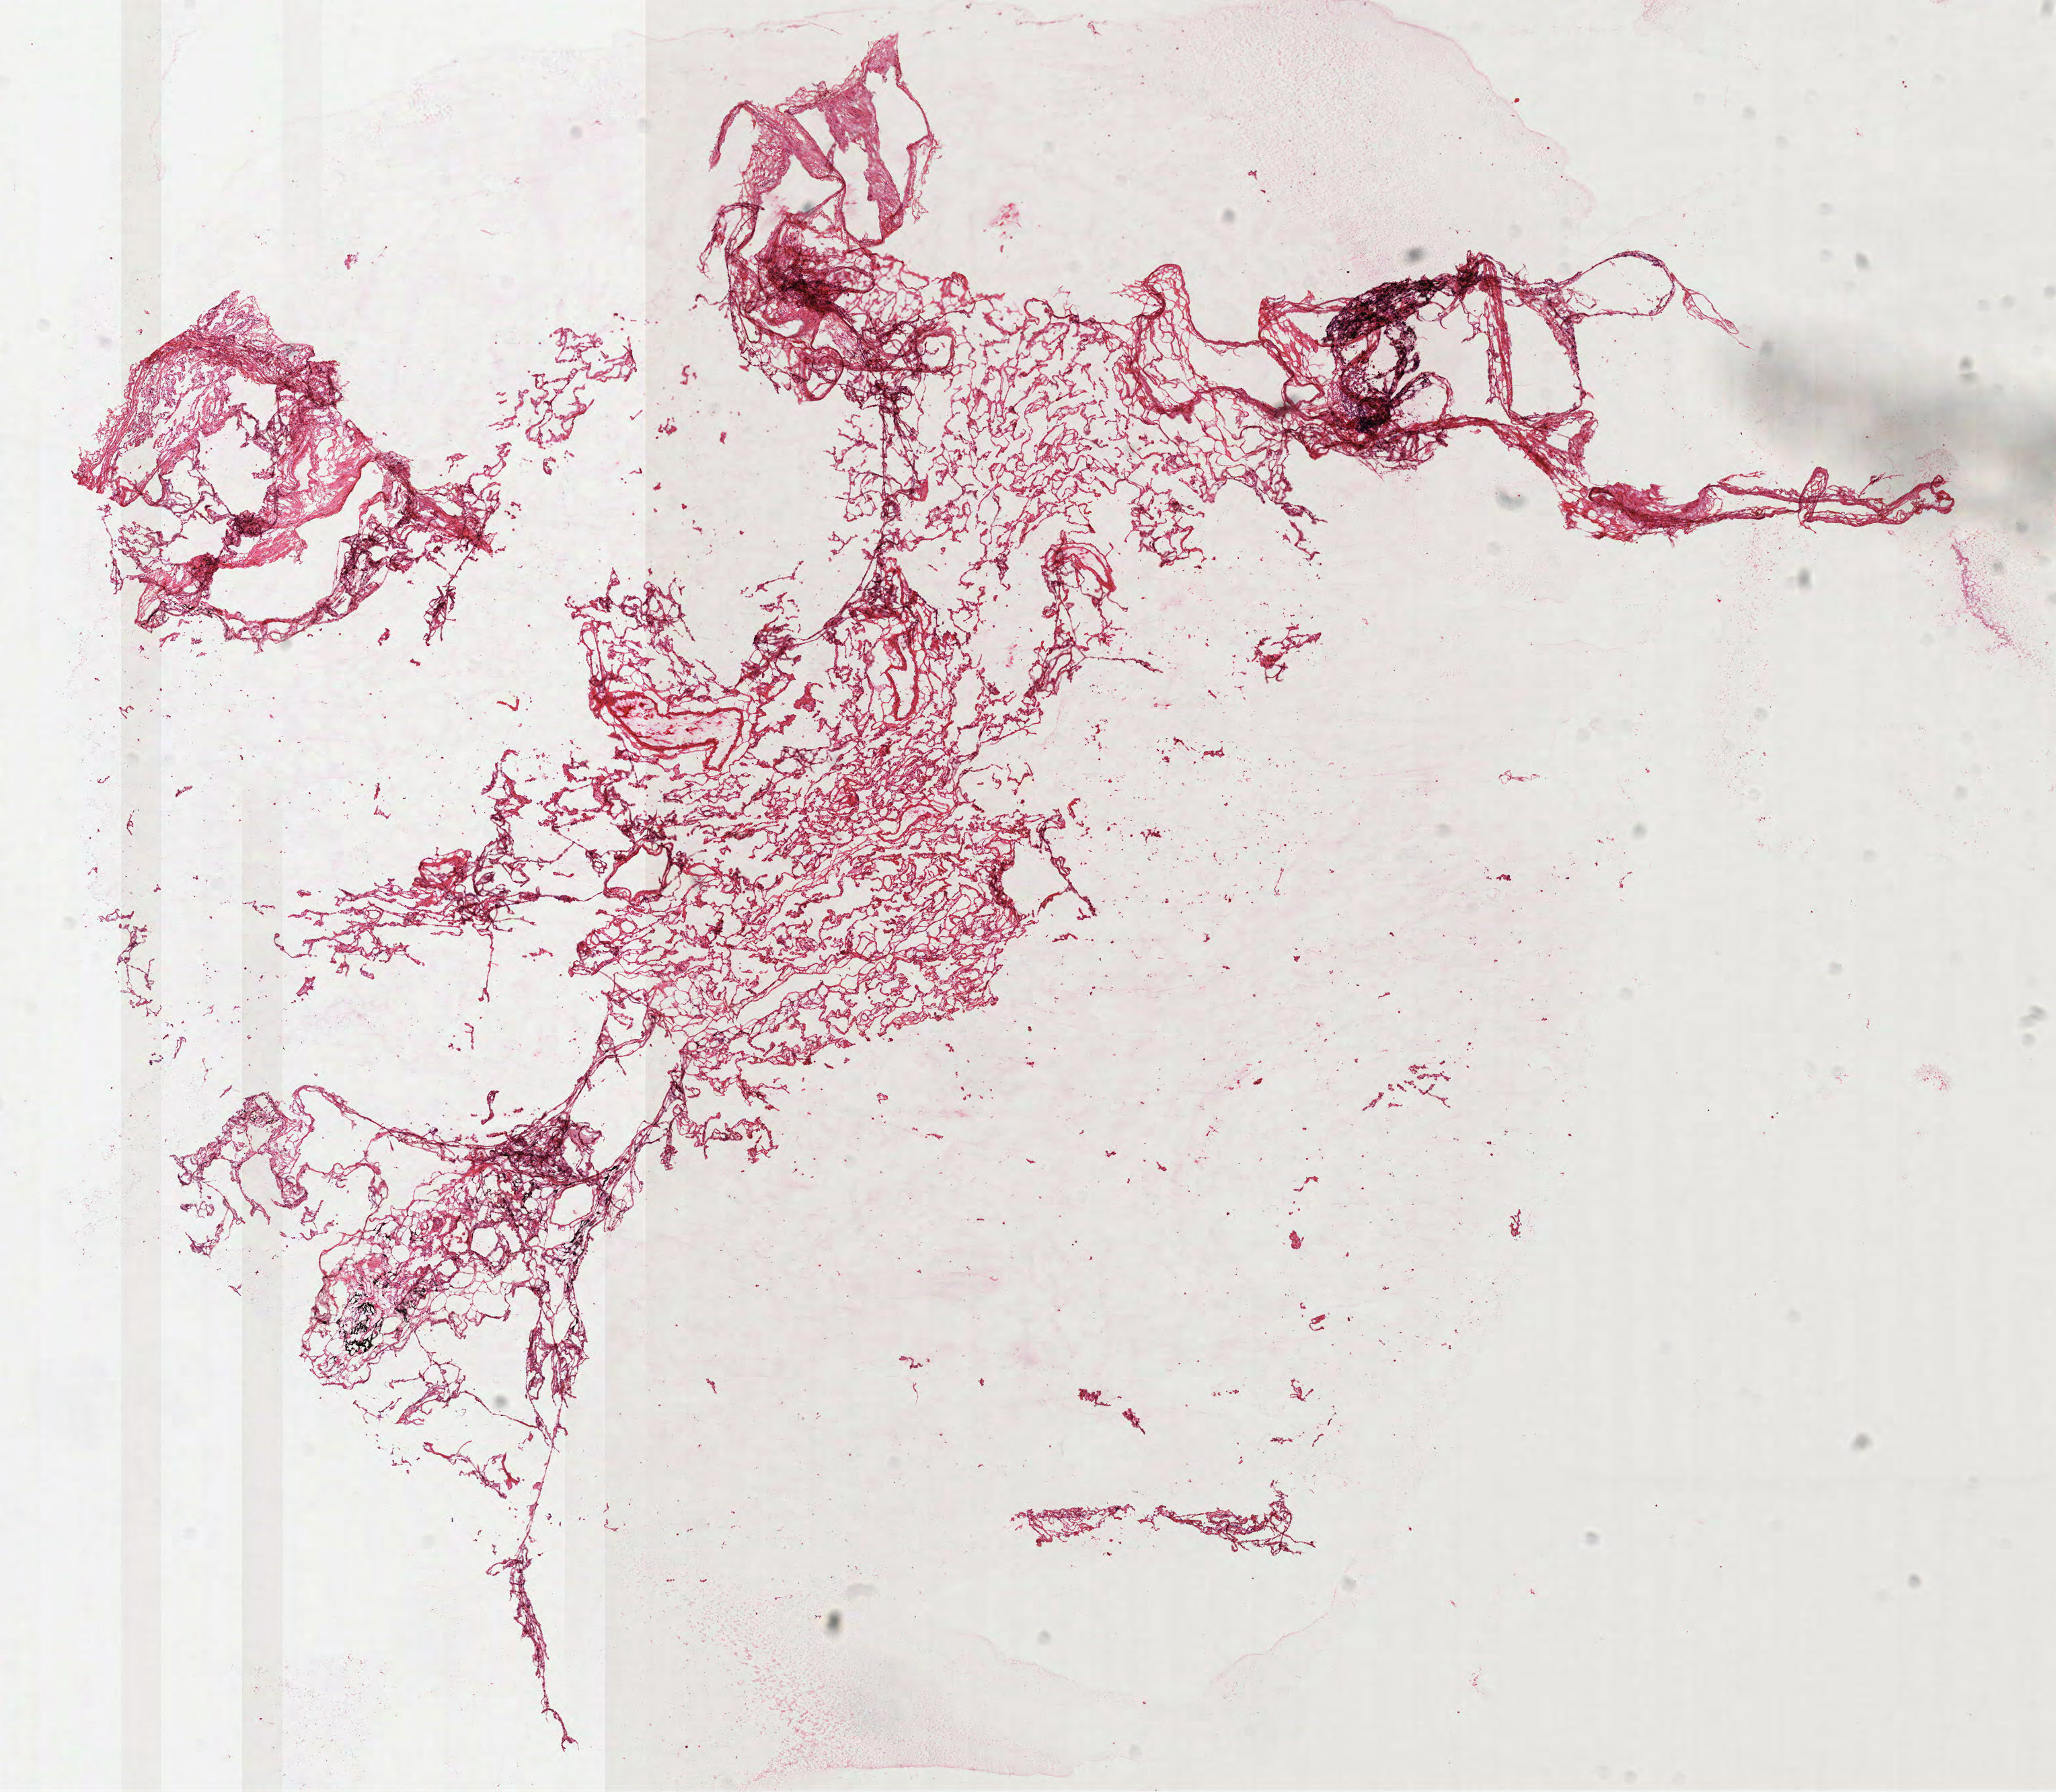
H&E whole-slide image, shown as a low-resolution overview of the whole scanned area (about 12.3 x 10.7 mm); frozen section from the top of the tissue portion; solid tissue normal (non-tumour tissue) sample from the lung. Female patient; age at initial diagnosis 62 years.
This section: solid tissue normal (non-tumour) sample from the same patient. Patient diagnosis: Squamous cell carcinoma, NOS (lower lobe, lung).